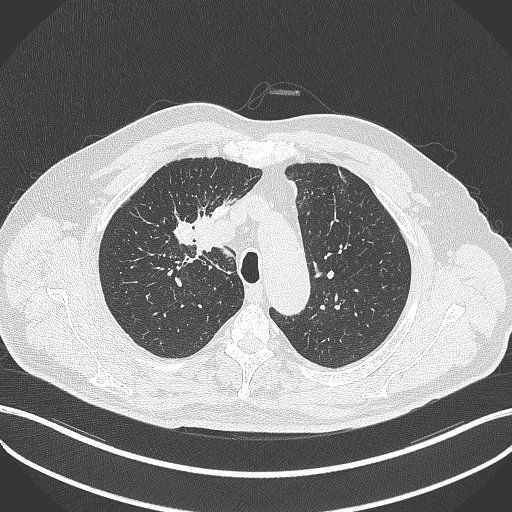
Chest CT, one axial slice. Position 299 of 411 along the scan axis. Reconstruction kernel B70f. 120 kVp. Lung window (W 1500 / L -600 HU). 512 × 512 image matrix, field of view 400 × 400 mm. Male patient, age 60 years. Case-level facts recorded for this patient, not image findings: clinical TNM (as recorded): T1b N1 M0.
Annotated regions visible in this slice (rectangle marked by the reading radiologist):
- lung tumour (recorded histology: squamous cell carcinoma): bounding box (x1, y1, x2, y2) in pixels: (190, 205, 219, 261)